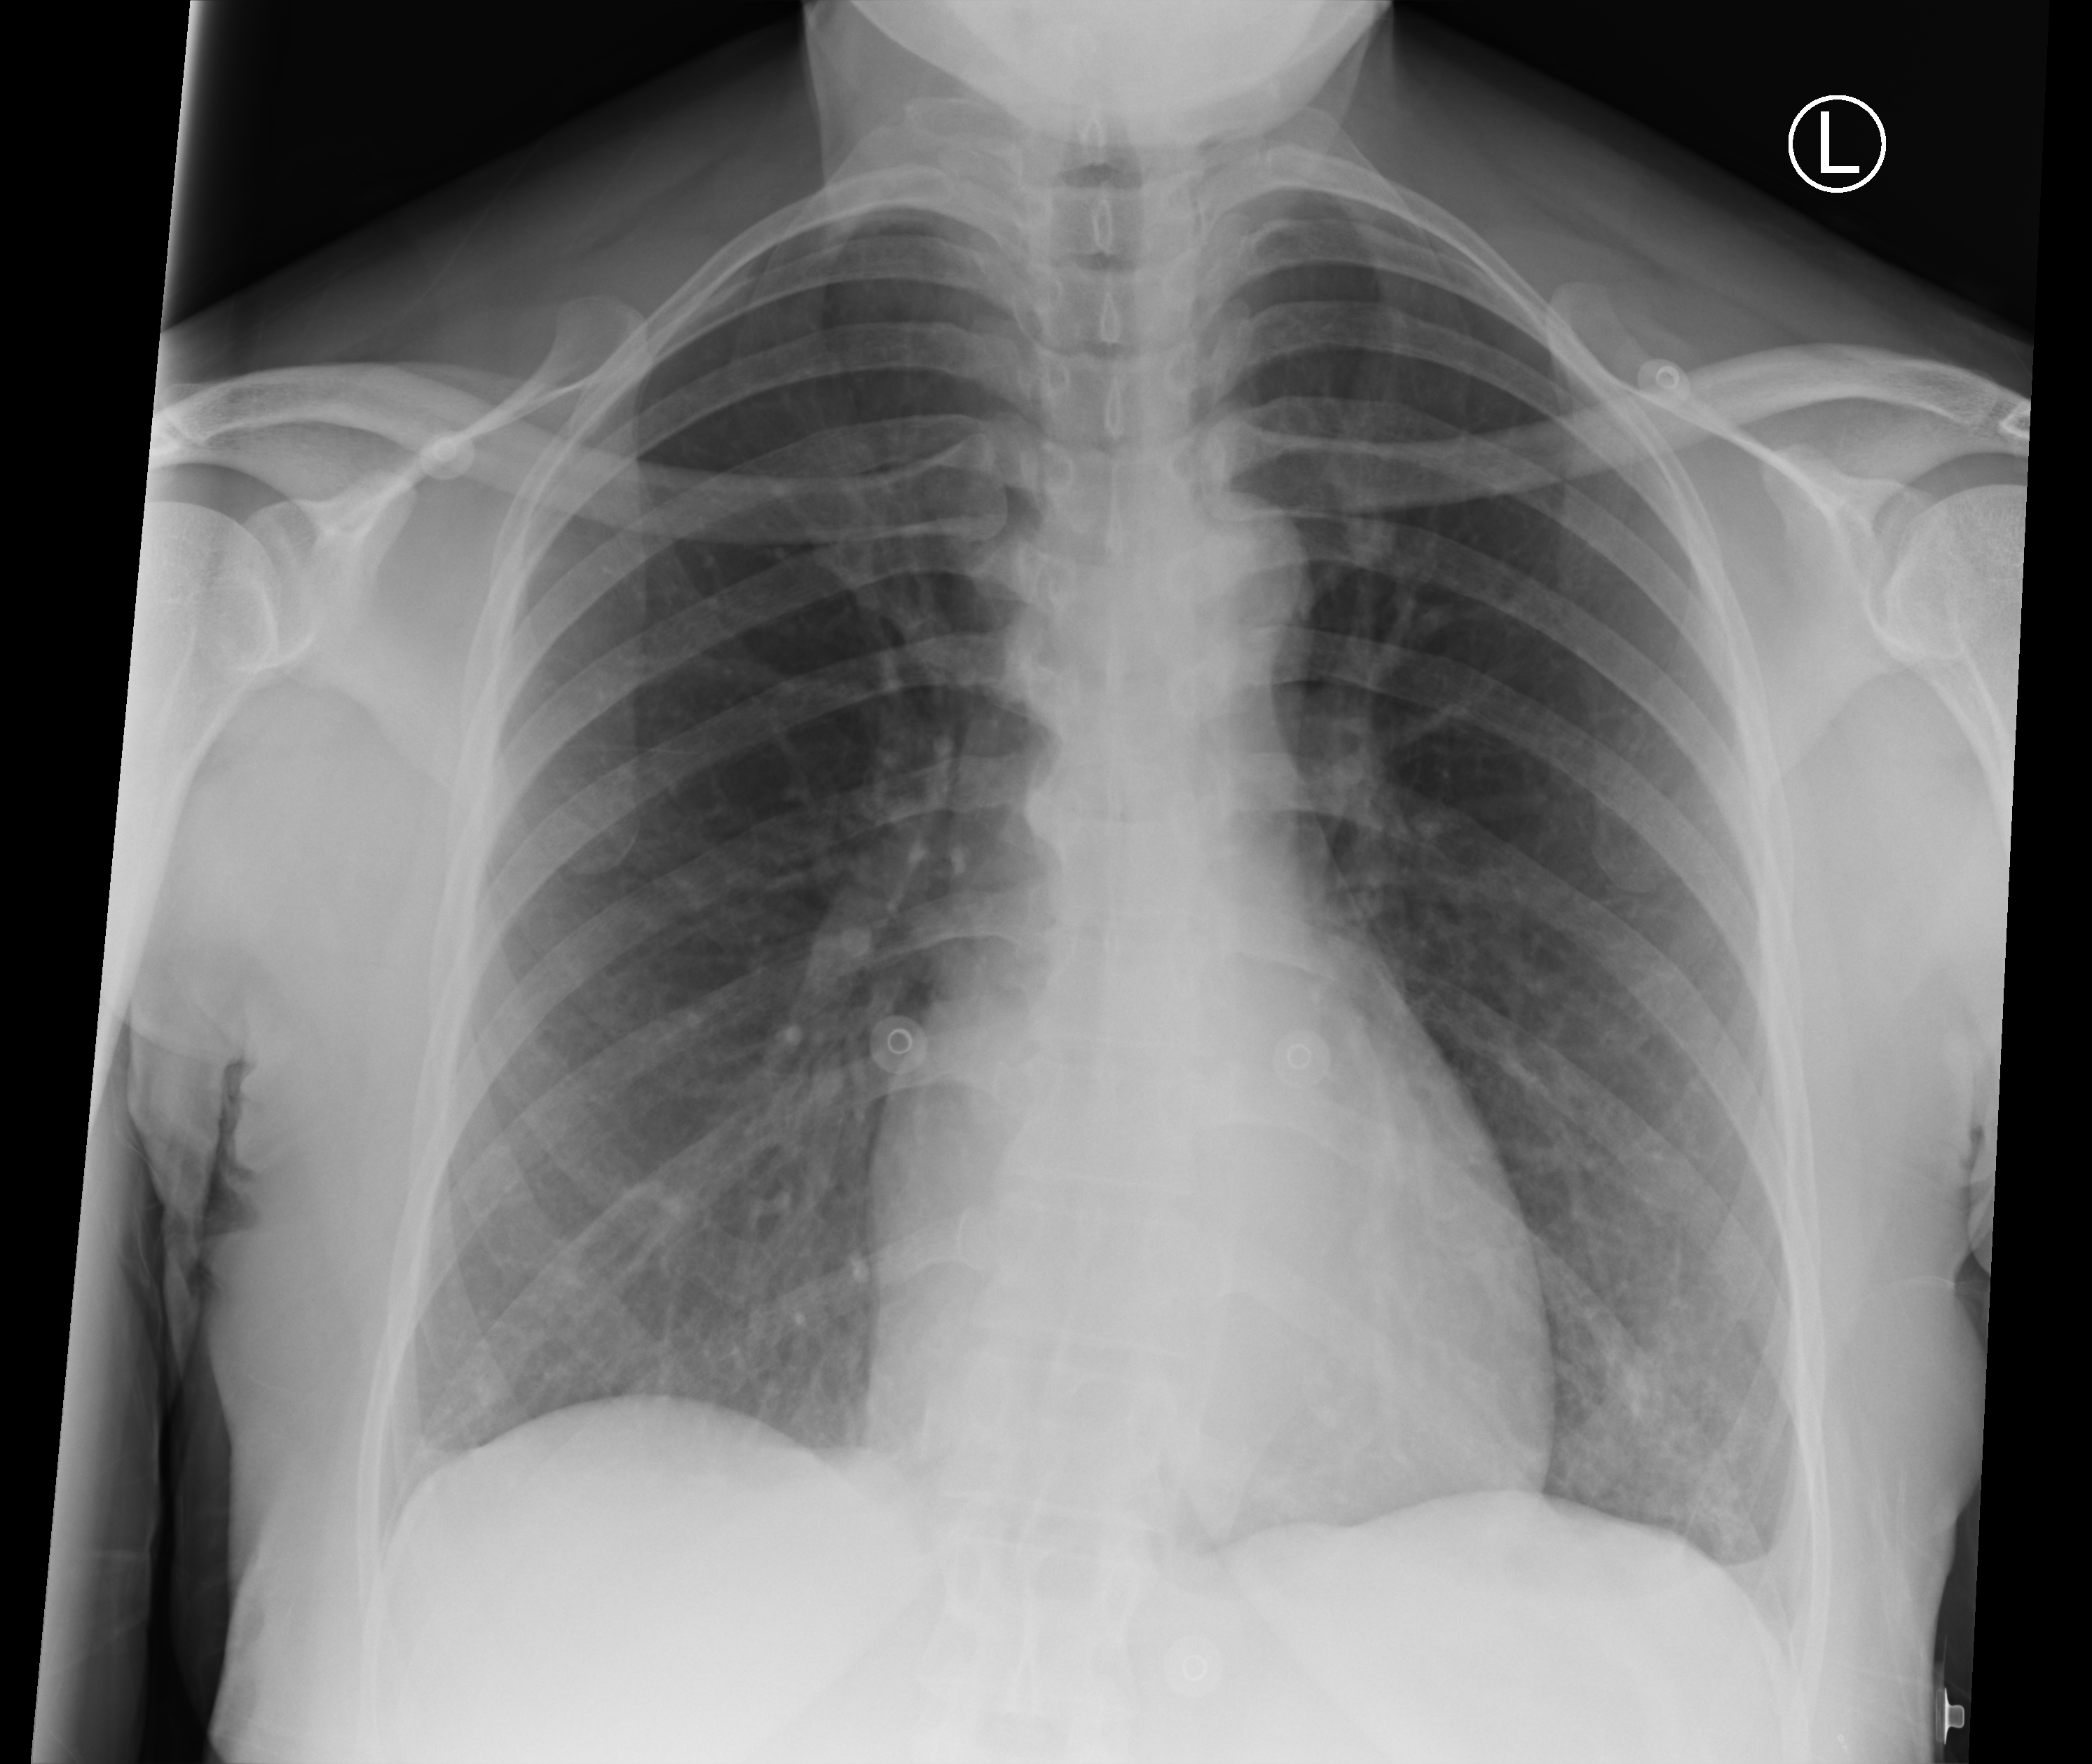
Bedside chest radiograph (computed radiography), anteroposterior (AP) projection. Patient hospitalised with COVID-19; female, aged 18–59 years.
From the hospital-stay record, not from the radiograph (when in the stay this image was taken is not recorded): admitted to intensive care during this hospital stay: no; COPD (admission record): no.